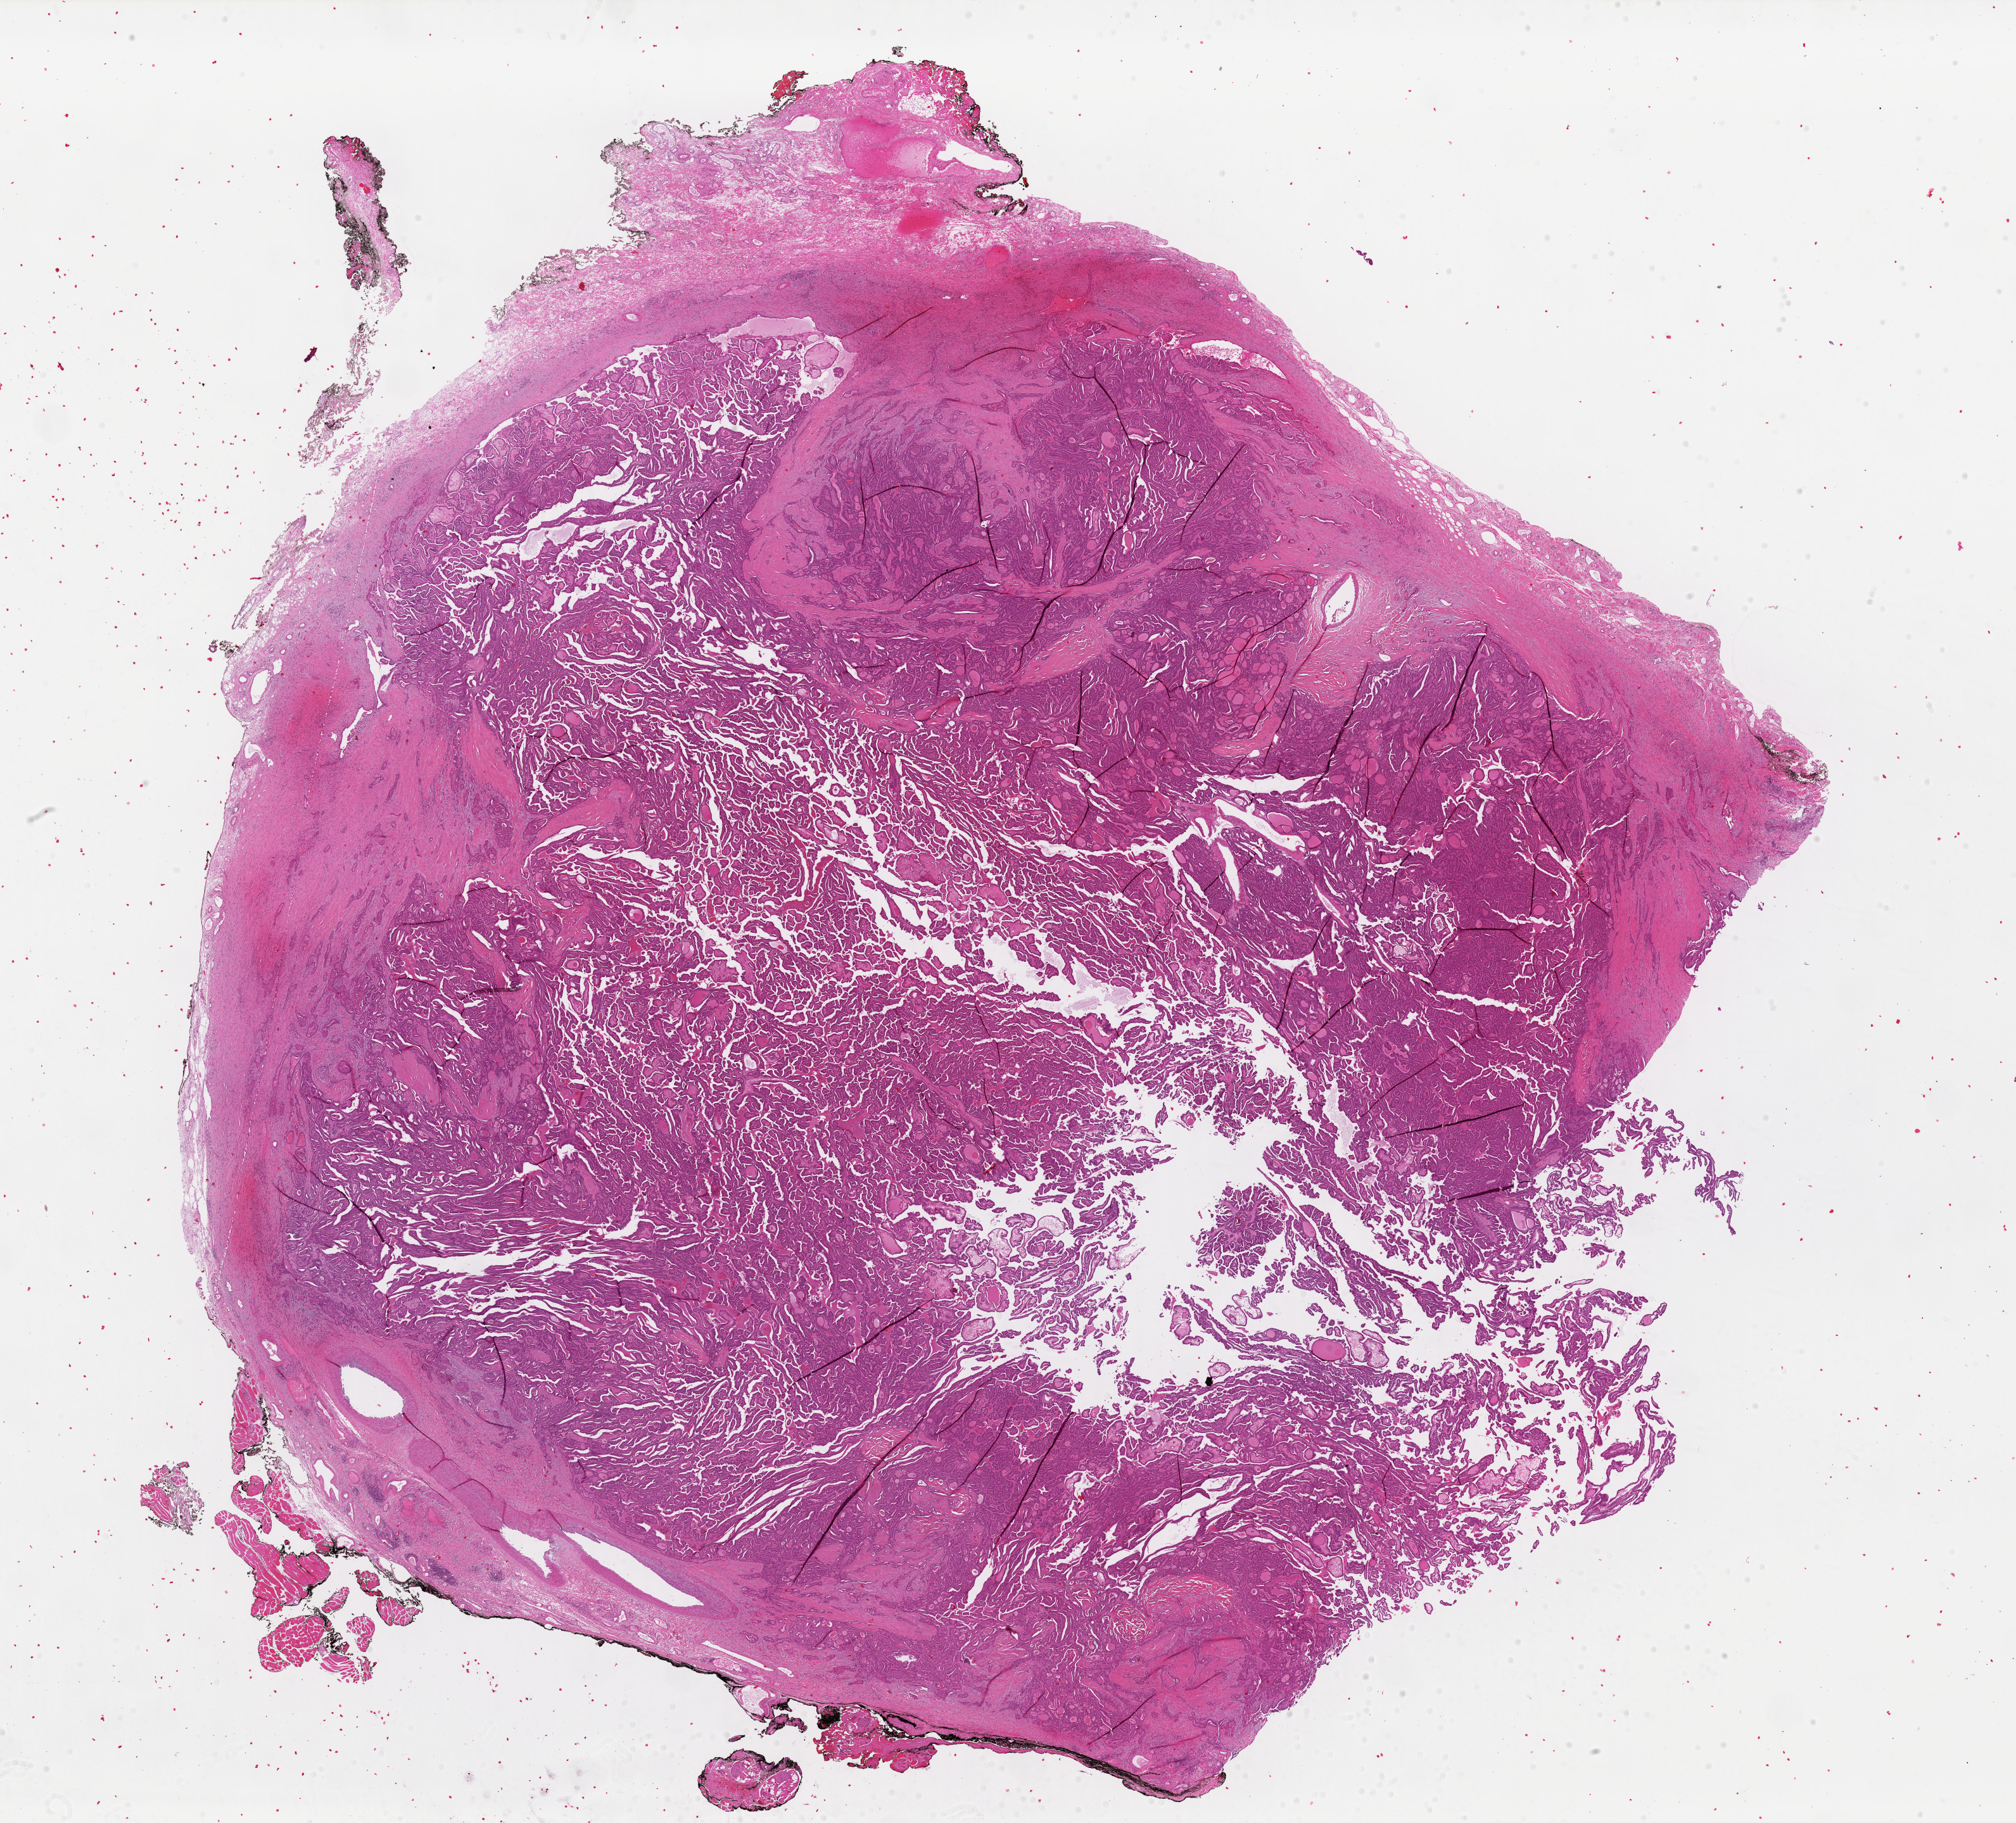
Digitized Hematoxylin and eosin (H&E) stained tissue section (whole slide), shown as a low-resolution overview of the whole scanned area (about 25.1 x 22.7 mm), FFPE section, sample: primary tumour, thyroid. Patient: female, age at initial diagnosis 52 years.
* AJCC pathologic stage: III (7th edition)
* TNM: T3 N1a M0
* pathologic diagnosis: Papillary adenocarcinoma, NOS (thyroid gland)